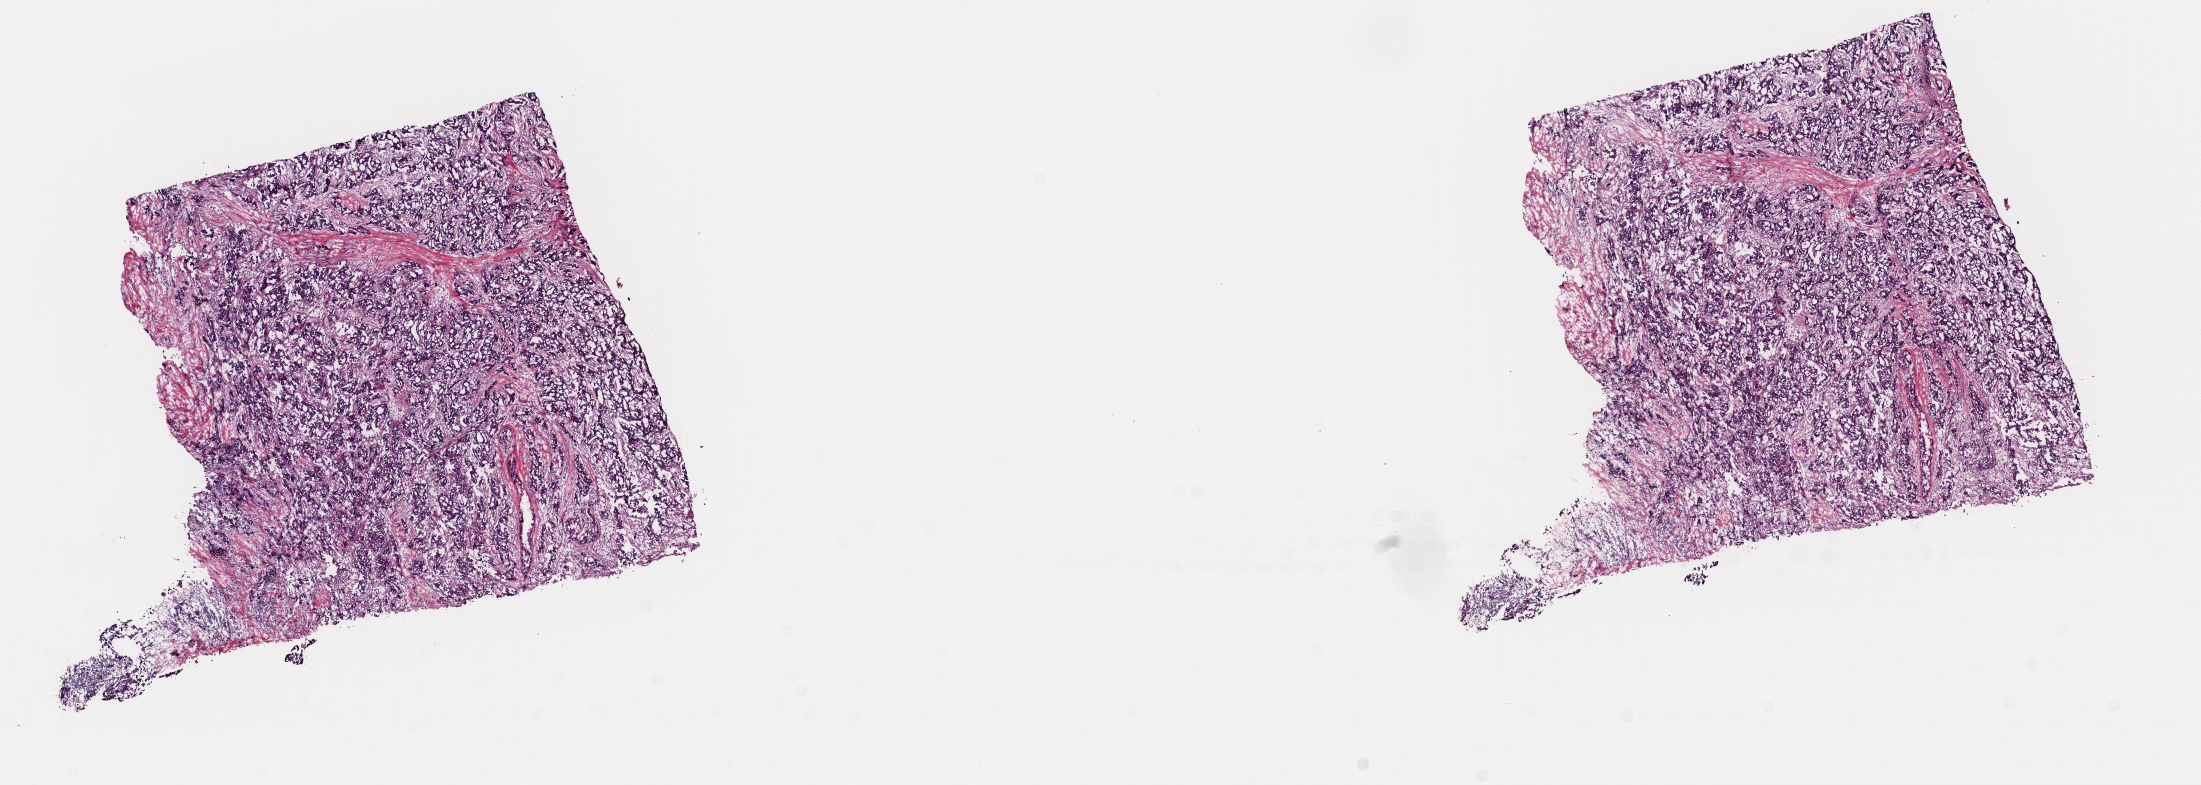
H&E whole-slide image — a low-resolution overview of the entire scanned area, about 17.4 x 6.2 mm (from a 40x scan), frozen section from the top of the tissue portion, sample: primary tumour, breast. Female patient; age at initial diagnosis 53 years. Pathologist review of this section (percent, as recorded): tumour cells 95%, tumour nuclei 80%, normal cells 0%, stromal cells 5%, necrosis 0%. Inflammatory infiltration, as recorded: lymphocyte infiltration 0%, monocyte infiltration 0%, neutrophil infiltration 0%.
AJCC pathologic stage: IIIA (7th edition). Lymph nodes positive (case pathology): 8 of 10 examined. Histologic diagnosis: Infiltrating duct carcinoma, NOS.